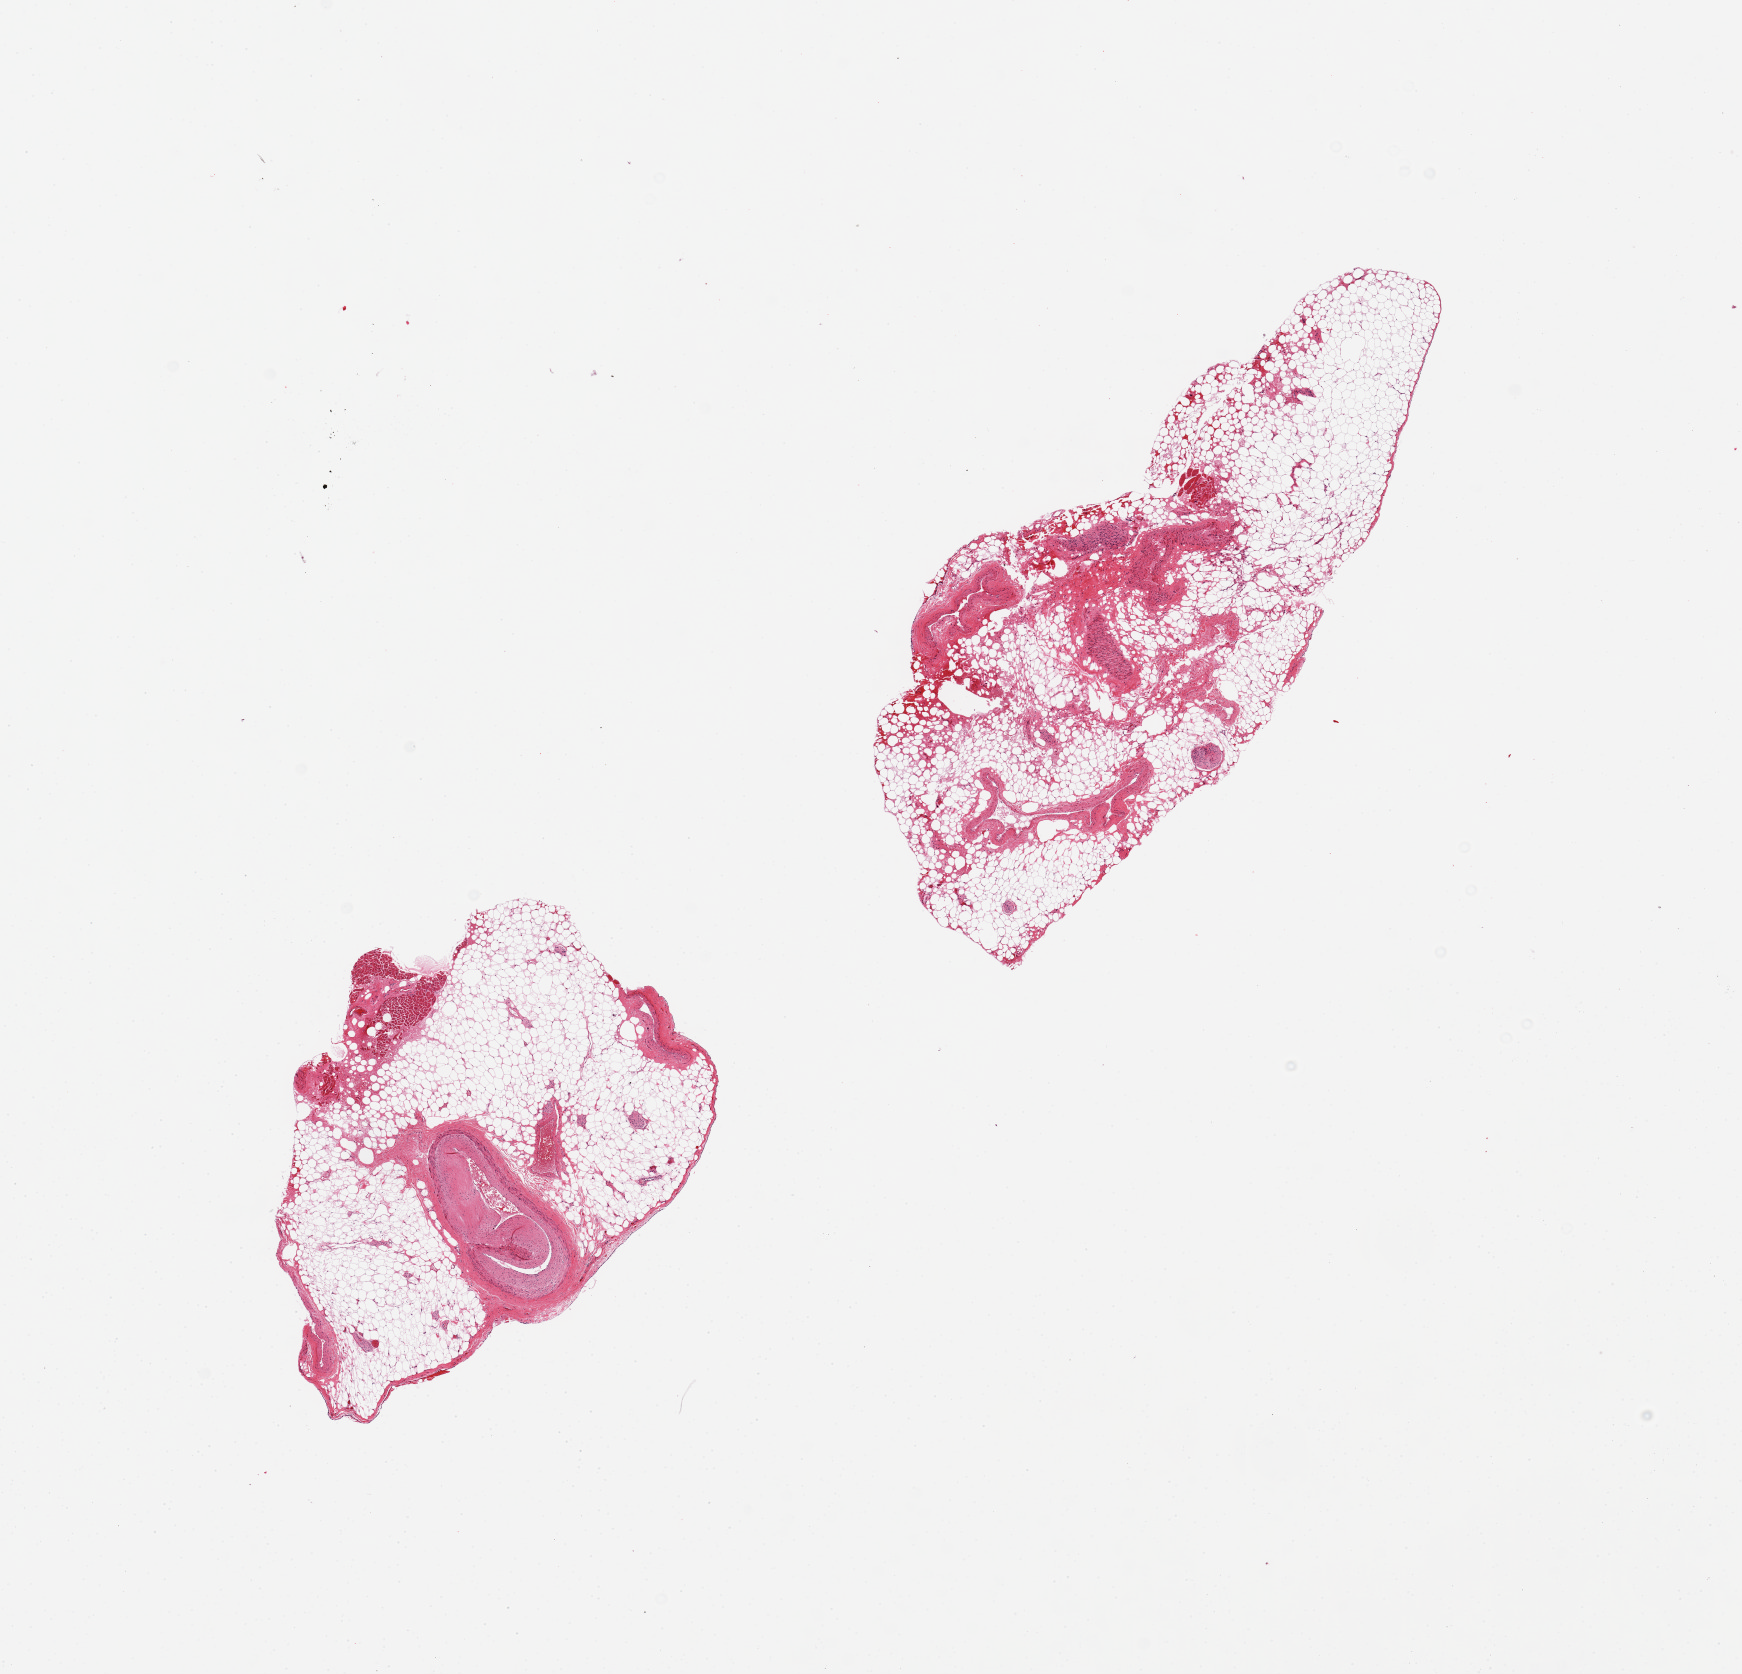
Whole-slide image, hematoxylin and eosin (H&E) stain, shown as a low-resolution overview of the whole scanned area (about 13.8 x 13.2 mm); PAXgene-fixed paraffin-embedded (PFPE) section; section of coronary artery (target tissue); donor tissue sample. Donor: male.
Reviewer comment on this tissue sample: 2 pieces, artery with atherosclerosis represents <10% of specimen which is predominantly fat with some cardiac muscle.